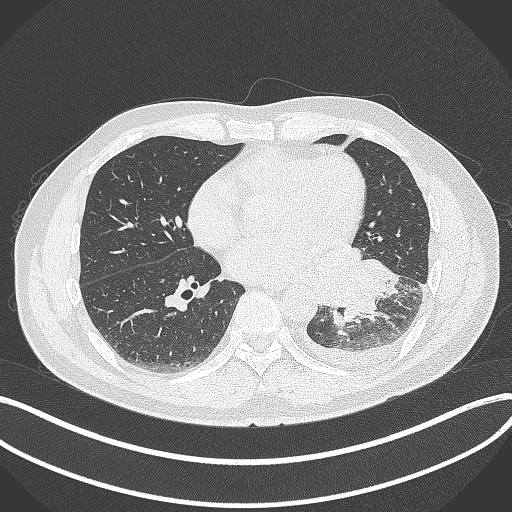
Chest CT, one axial slice; position 151 of 342 along the scan axis; 120 kVp; lung window (W 1500 / L -600 HU); 1 mm slice thickness; 512 × 512 image matrix. Patient: male, 58 years. From the clinical record (not read from this slice): clinical TNM (as recorded): T3 N1 M1b; histopathological grade: G3.
Structures marked on this image (rectangle marked by the reading radiologist):
- lung tumour (recorded histology: small cell carcinoma): bounding box [x1, y1, x2, y2] px = [308, 235, 401, 323]